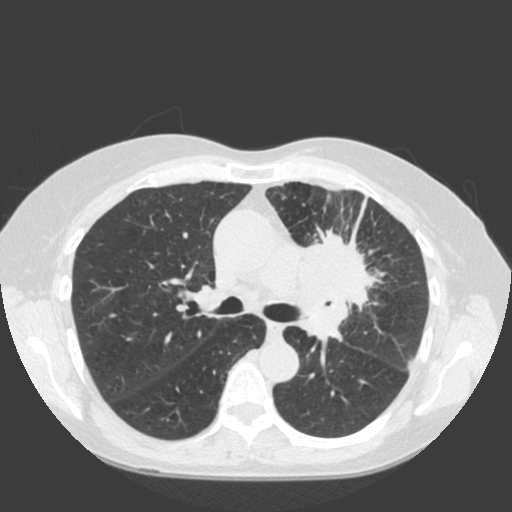
Low-dose screening chest CT, one axial slice; slice 120 of 184 in the series (ordered by position); lung window (W 1500 / L -600 HU); 2 mm slice thickness; 512 × 512 image matrix.
Structures marked on this image (outlined manually by an expert reader):
- lesion 1 (tumor, hilum of left lung): bounding box <296,231,381,341> (left, top, right, bottom; pixels)